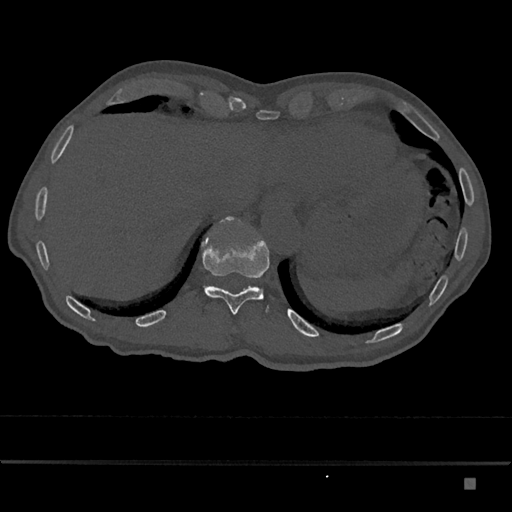
CT including the spine, one axial slice. Position 672 of 797 along the scan axis. Reconstruction kernel Br40s/3. Bone window (W 1800 / L 400 HU). 0.5 mm slice thickness. 512 × 512 image matrix, field of view 390 × 390 mm. Patient: male, 72 years. Case-level facts recorded for this patient, not image findings: primary cancer: prostate.
Outlined on this slice (semi-automatically segmented with operator editing):
- T11 vertebra: bounding box (x1, y1, x2, y2) in pixels: (201, 216, 270, 315)